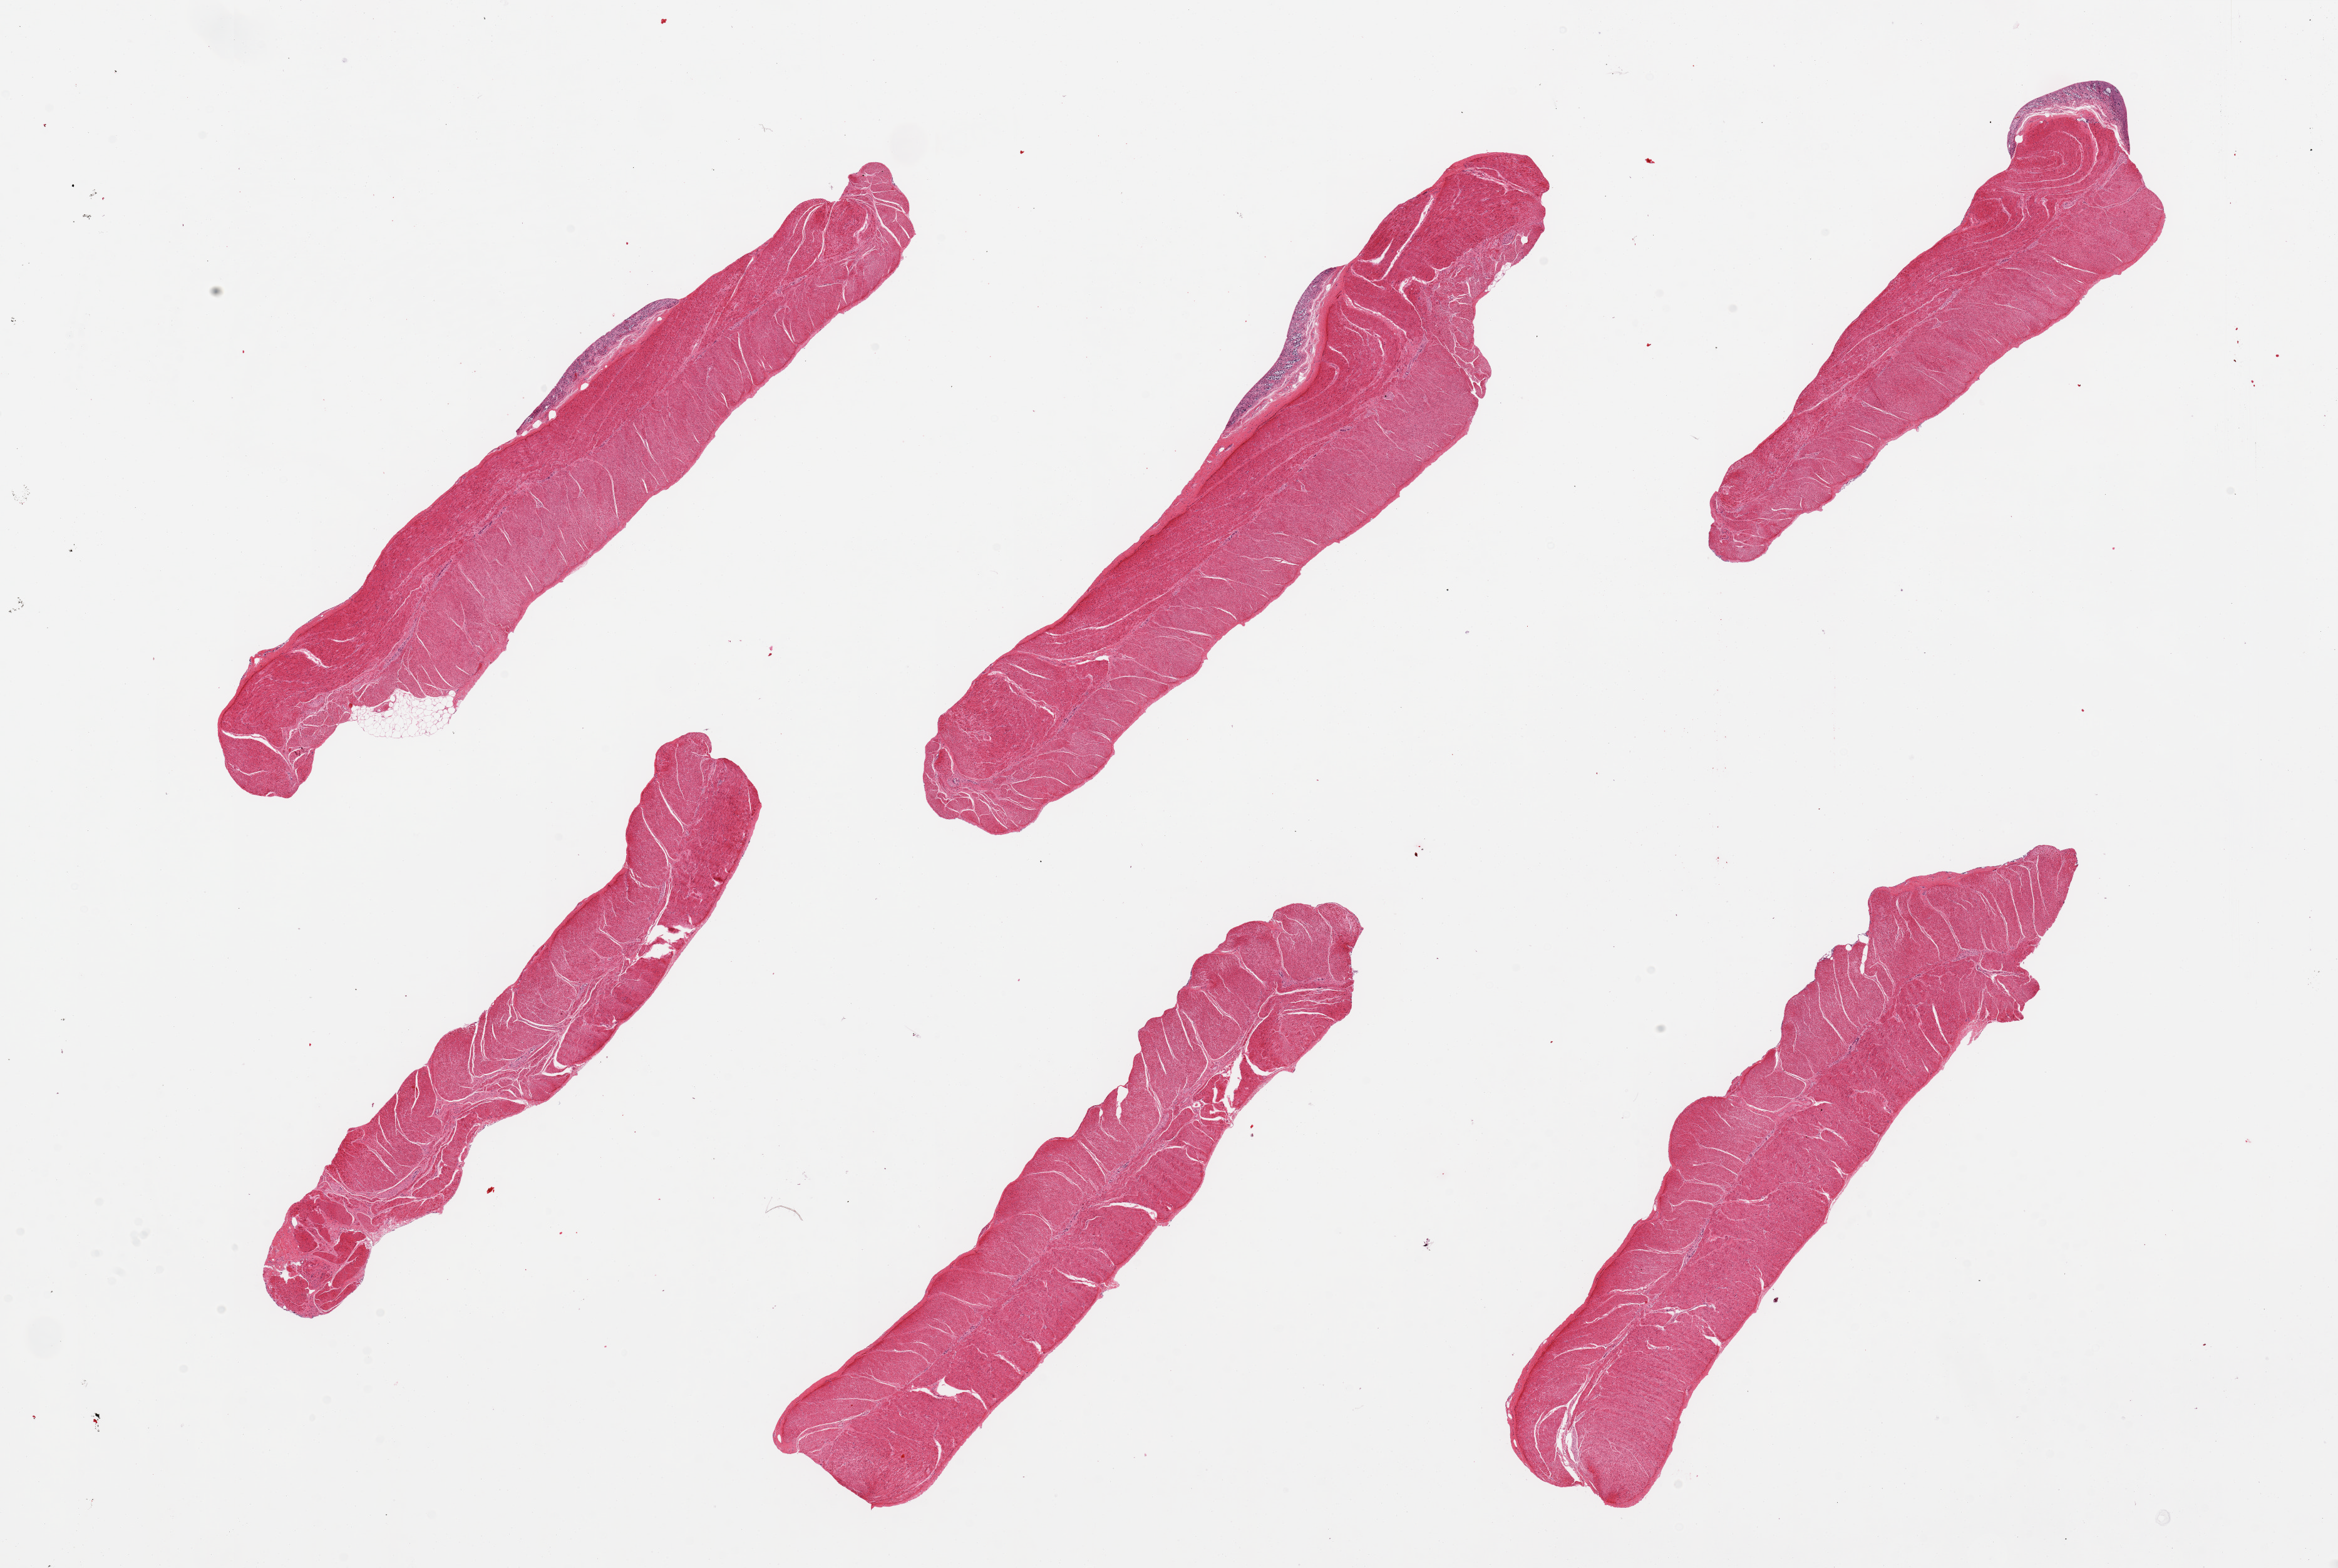
Digitized H&E-stained section — a low-resolution overview of the entire scanned area, about 29.5 x 19.8 mm, PAXgene-fixed paraffin-embedded (PFPE) section, sampled site (target tissue): sigmoid colon, donor tissue sample. Donor: male.
Reviewer comment on this tissue sample: 6 pieces; 3 have small autolyzed mucosal remnants, otherwise well trimmed muscularis.